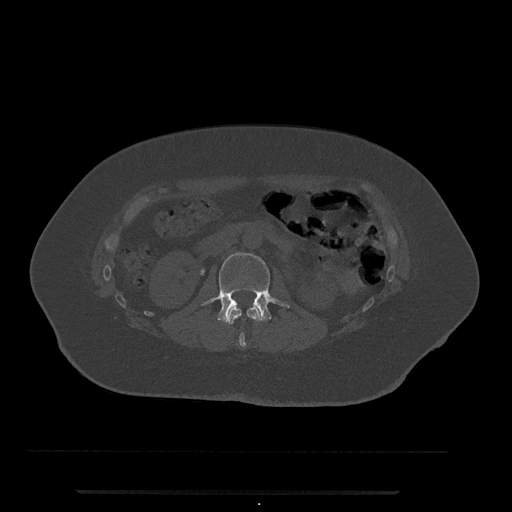
CT including the spine, one axial slice. Slice 56 of 797 in the series (ordered by position). Reconstruction kernel Br40s/3. 120 kVp. Bone window (W 1800 / L 400 HU). 0.5 mm slice thickness. 512 × 512 image matrix. Female patient, age 51 years. From the clinical record (not read from this slice): primary cancer: neuro.
Outlined on this slice (semi-automatic segmentation, software-assisted and operator-edited):
- L1 vertebra: bounding box [x1, y1, x2, y2] px = [226, 307, 261, 347]
- L2 vertebra: [202, 252, 290, 323]